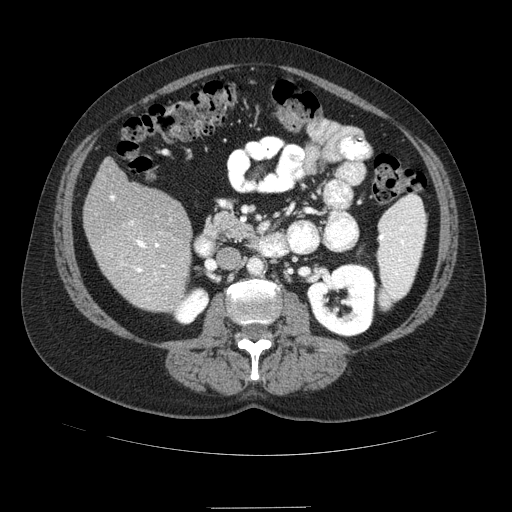
Contrast-enhanced abdominal CT (liver protocol), one axial slice. Slice 29 of 89 in the series (ordered by position). Reconstruction kernel STANDARD. Soft-tissue window (W 400 / L 40 HU). 2.5 mm slice thickness. 512 × 512 image matrix, field of view 400 × 400 mm. From the clinical record (not read from this slice): diagnosis: hepatocellular carcinoma (patient treated with transarterial chemoembolisation; whether this scan precedes or follows treatment is not stated here); TNM stage (as recorded): Stage-IIIB; Child-Pugh class: A; tumour nodularity: multinodular.
Outlined on this slice (semi-automatically segmented with operator editing):
- liver parenchyma outside the tumour (the mass and vessels are separate outlines, so this box may not span the whole liver): bounding box (x1, y1, x2, y2) in pixels: (84, 158, 192, 310)
- liver vessels: (110, 195, 168, 288)